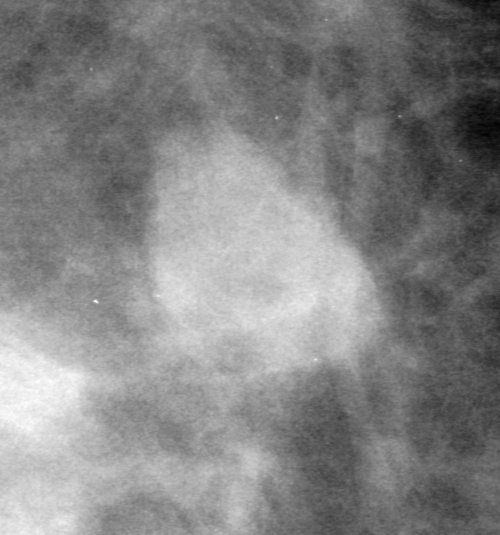
Crop from a digitized film mammogram around one marked abnormality; left breast; MLO view; BI-RADS breast density category 2 (scale 1–4).
- Marked abnormality: mass, shape irregular, margins ill defined; BI-RADS assessment category 0 (incomplete: needs additional imaging); pathology result (as recorded, not read from the image): benign.